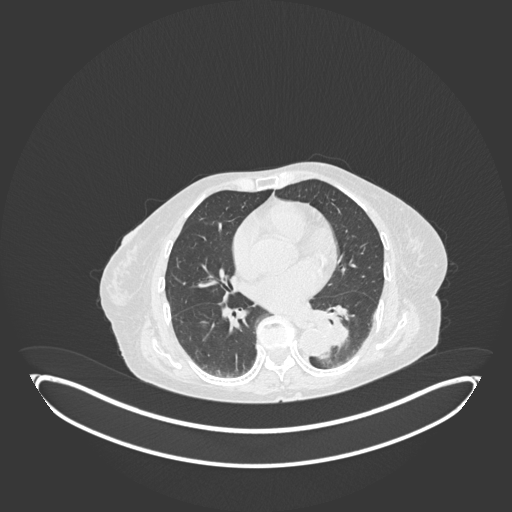
Chest CT, one axial slice; slice 52 of 189 in the series (ordered by position); reconstruction kernel B30f; lung window (W 1500 / L -600 HU); 1 mm slice thickness; 512 × 512 image matrix, field of view 500 × 500 mm. Patient: female, 82 years. From the clinical record (not read from this slice): clinical TNM (as recorded): T1b N0 M1.
Structures marked on this image (bounding box drawn by a radiologist):
- lung tumour (recorded histology: adenocarcinoma): bounding box (x1, y1, x2, y2) in pixels: (314, 311, 355, 351)